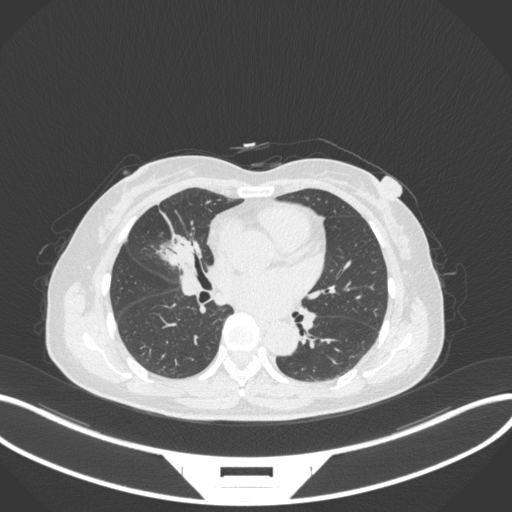
Chest CT, one axial slice; slice 151 of 282 in the series (ordered by position); reconstruction kernel B31f; 120 kVp; lung window (W 1500 / L -600 HU); 1 mm slice thickness; 512 × 512 image matrix, field of view 400 × 400 mm. Female patient, age 51 years. Case-level facts recorded for this patient, not image findings: clinical TNM (as recorded): T1c N0 M0; histopathological grade: G2.
Annotated regions visible in this slice (bounding box drawn by a radiologist):
- lung tumour (recorded histology: adenocarcinoma): bounding box <150,226,202,273> (left, top, right, bottom; pixels)